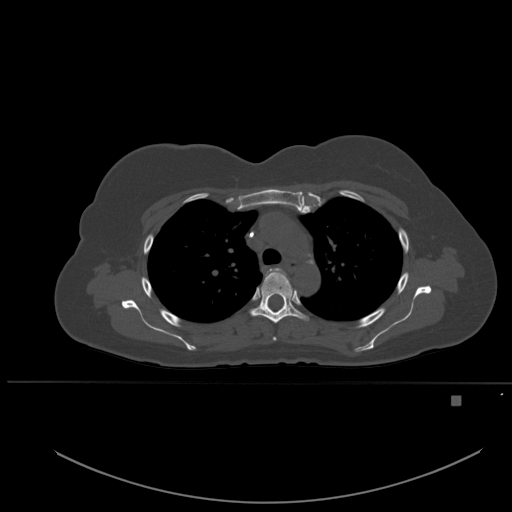
CT including the spine, one axial slice. Position 381 of 651 along the scan axis. Bone window (W 1800 / L 400 HU). 512 × 512 image matrix. Female patient, age 49 years. Case-level facts recorded for this patient, not image findings: primary cancer: breast.
Annotated regions visible in this slice (semi-automatically segmented with operator editing):
- T3 vertebra: bounding box [x1, y1, x2, y2] px = [270, 268, 281, 341]
- T4 vertebra: [251, 271, 308, 324]